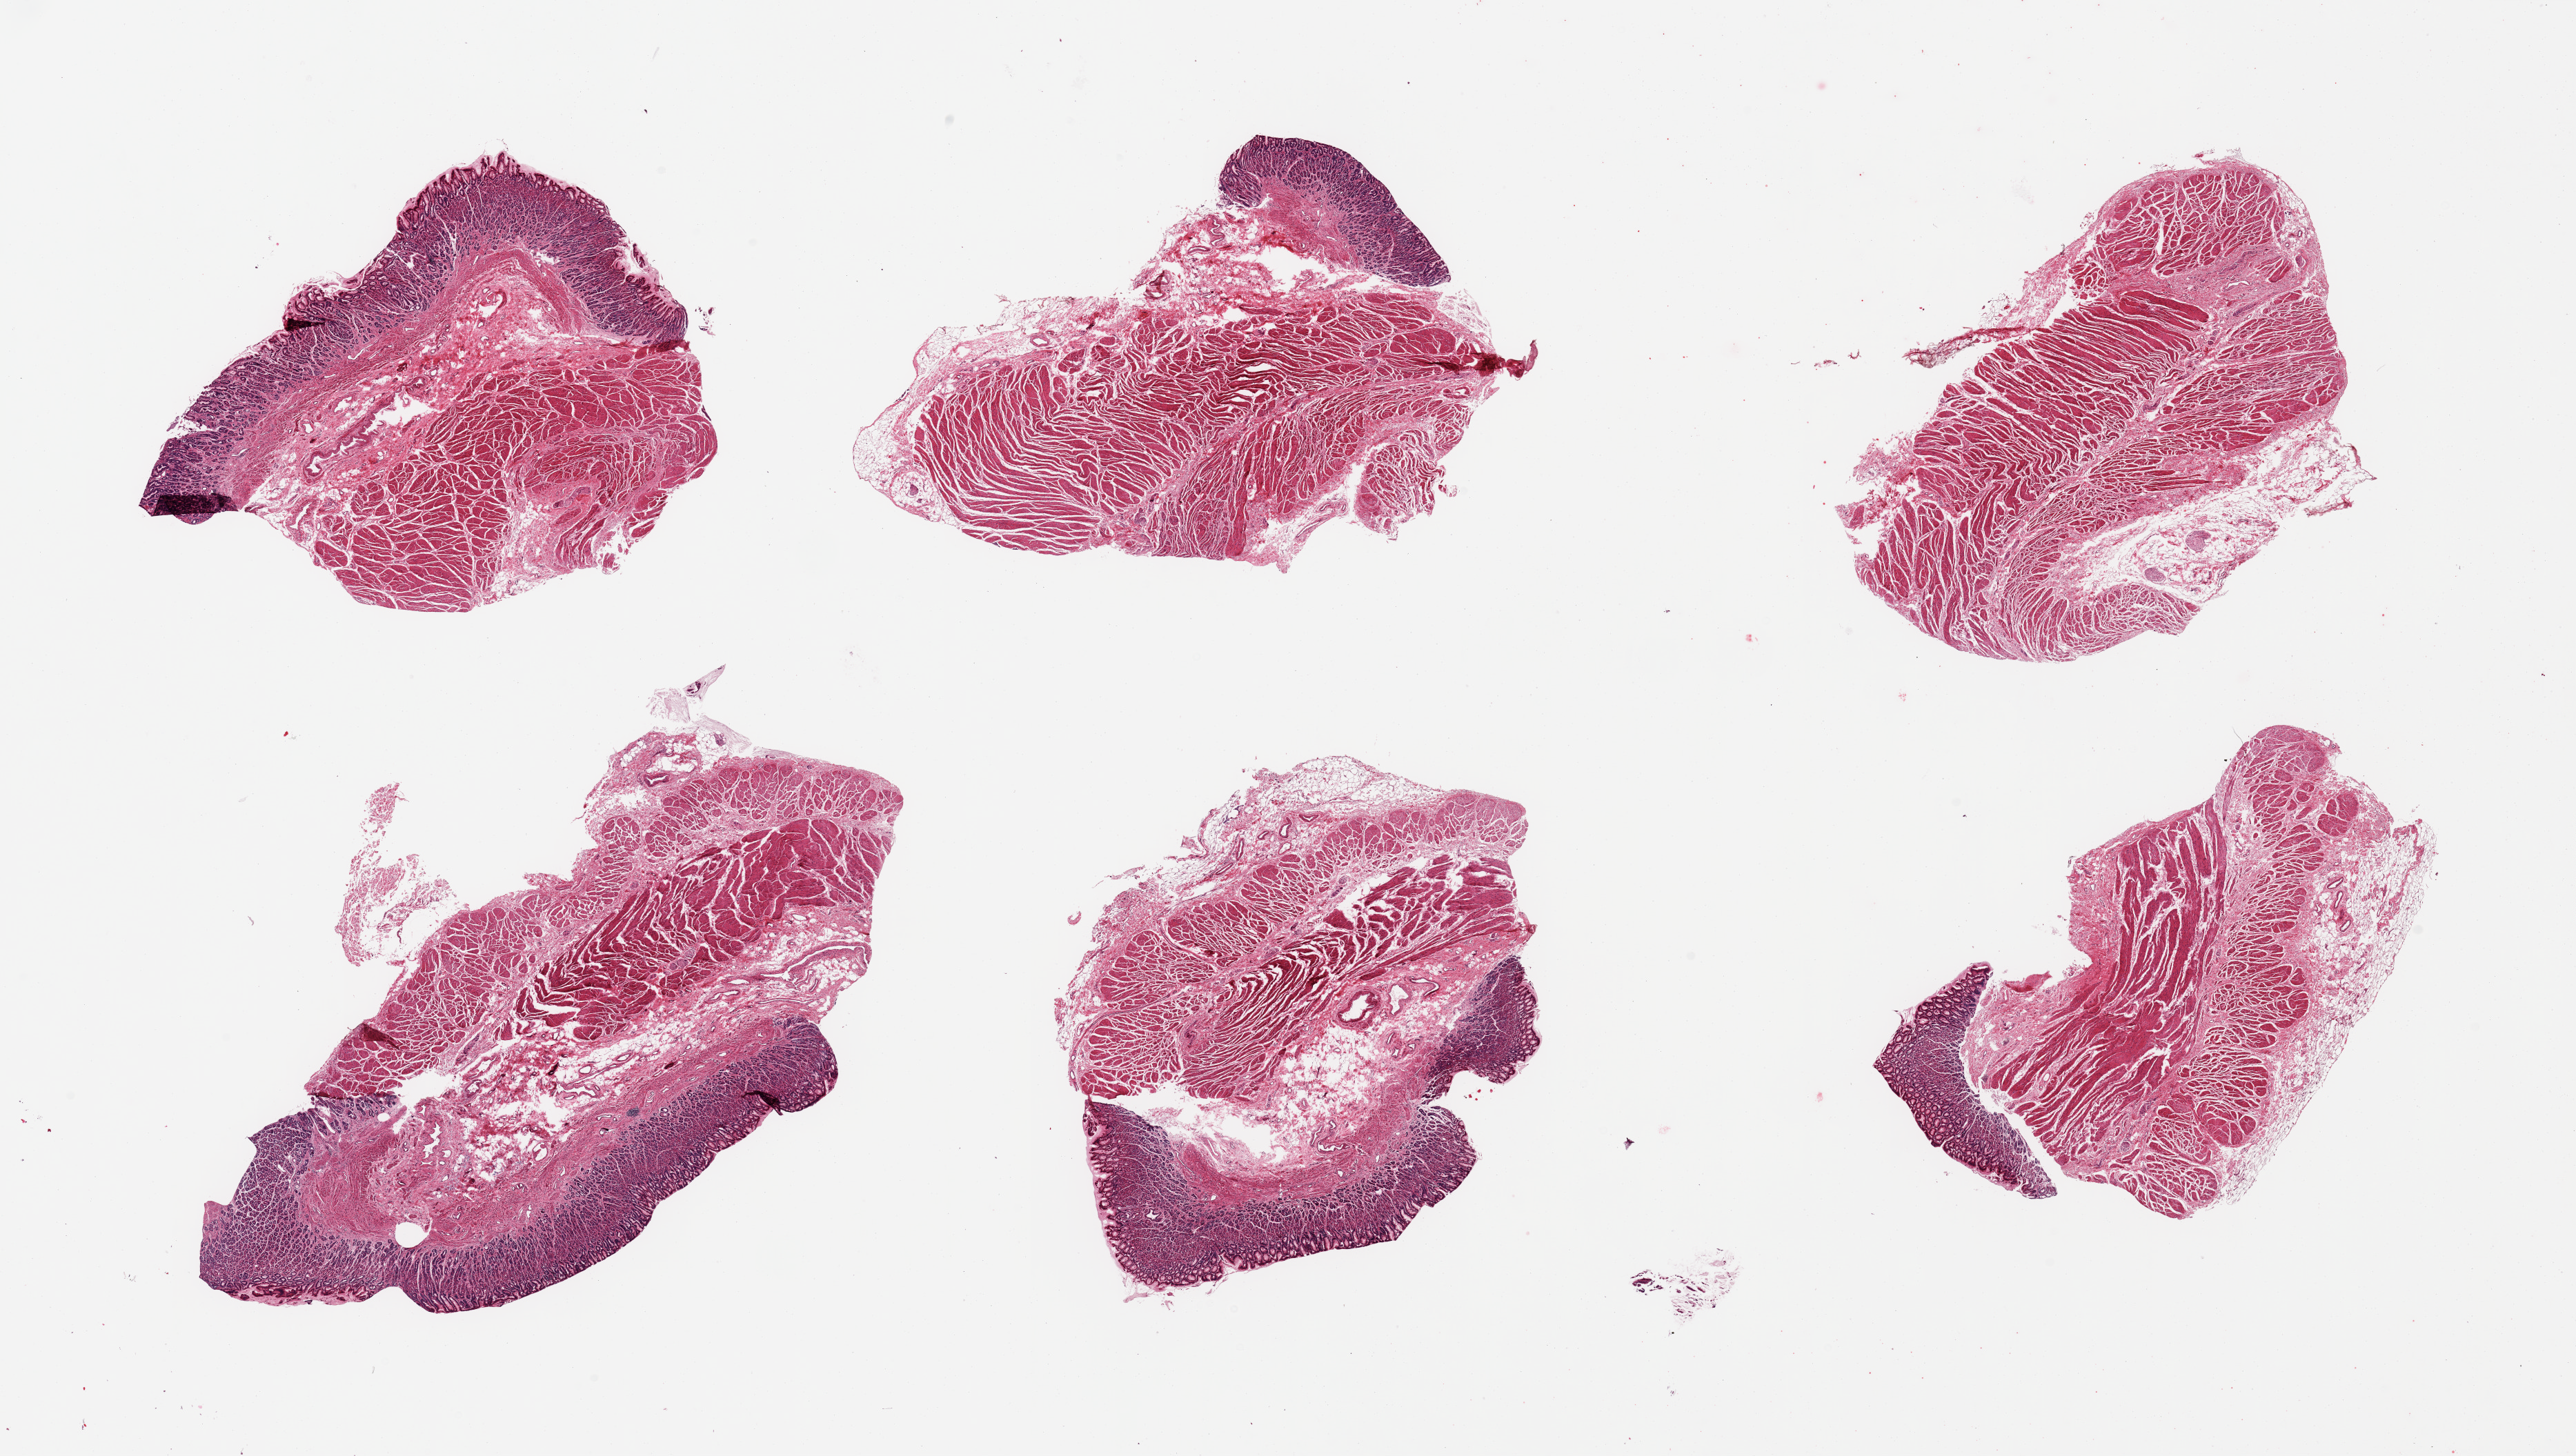
Digitized hematoxylin and eosin (H&E)-stained section, whole scanned area (about 29.5 x 16.7 mm, from a 20x scan) shown as a low-resolution overview. Male donor.
Specimen: PAXgene-fixed paraffin-embedded (PFPE) section; section of gastroesophageal junction (target tissue); donor tissue sample.